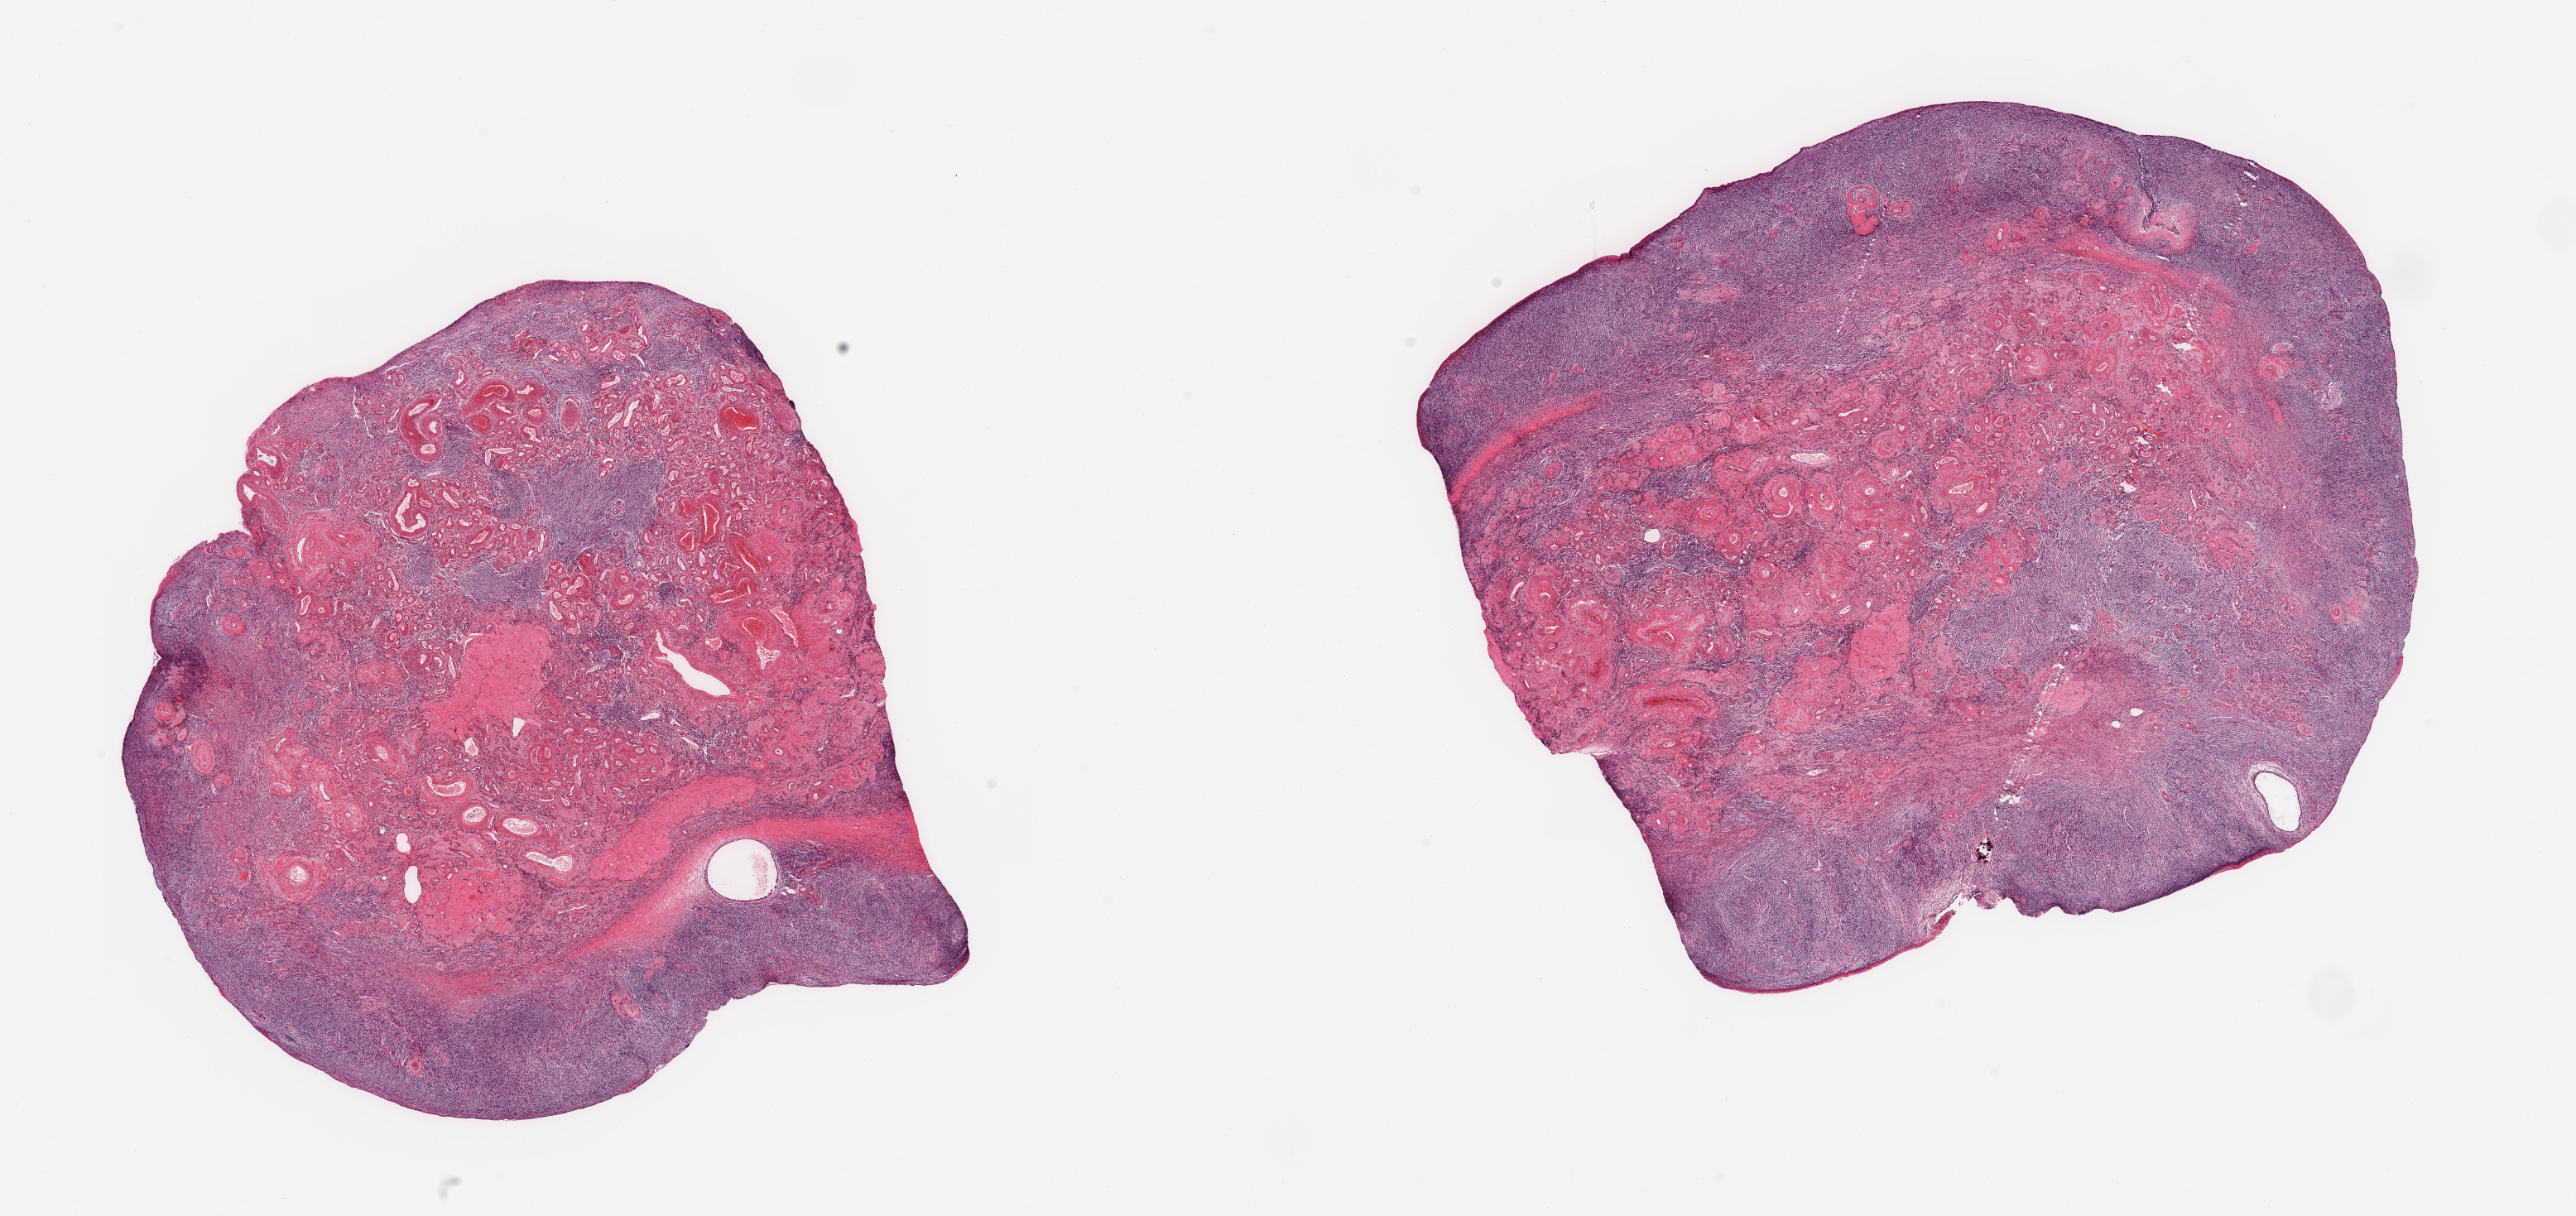
Digitized haematoxylin and eosin-stained section, brightfield — shown as a low-resolution overview of the whole scanned area (about 24.6 x 11.6 mm), PAXgene-fixed, paraffin-embedded tissue, section of ovary (target tissue), donor tissue sample. Donor sex: female.
Reviewer comment on this tissue sample: 2 pieces; largely hilum/vessels, ovarian stroma with corpora fibrosa.